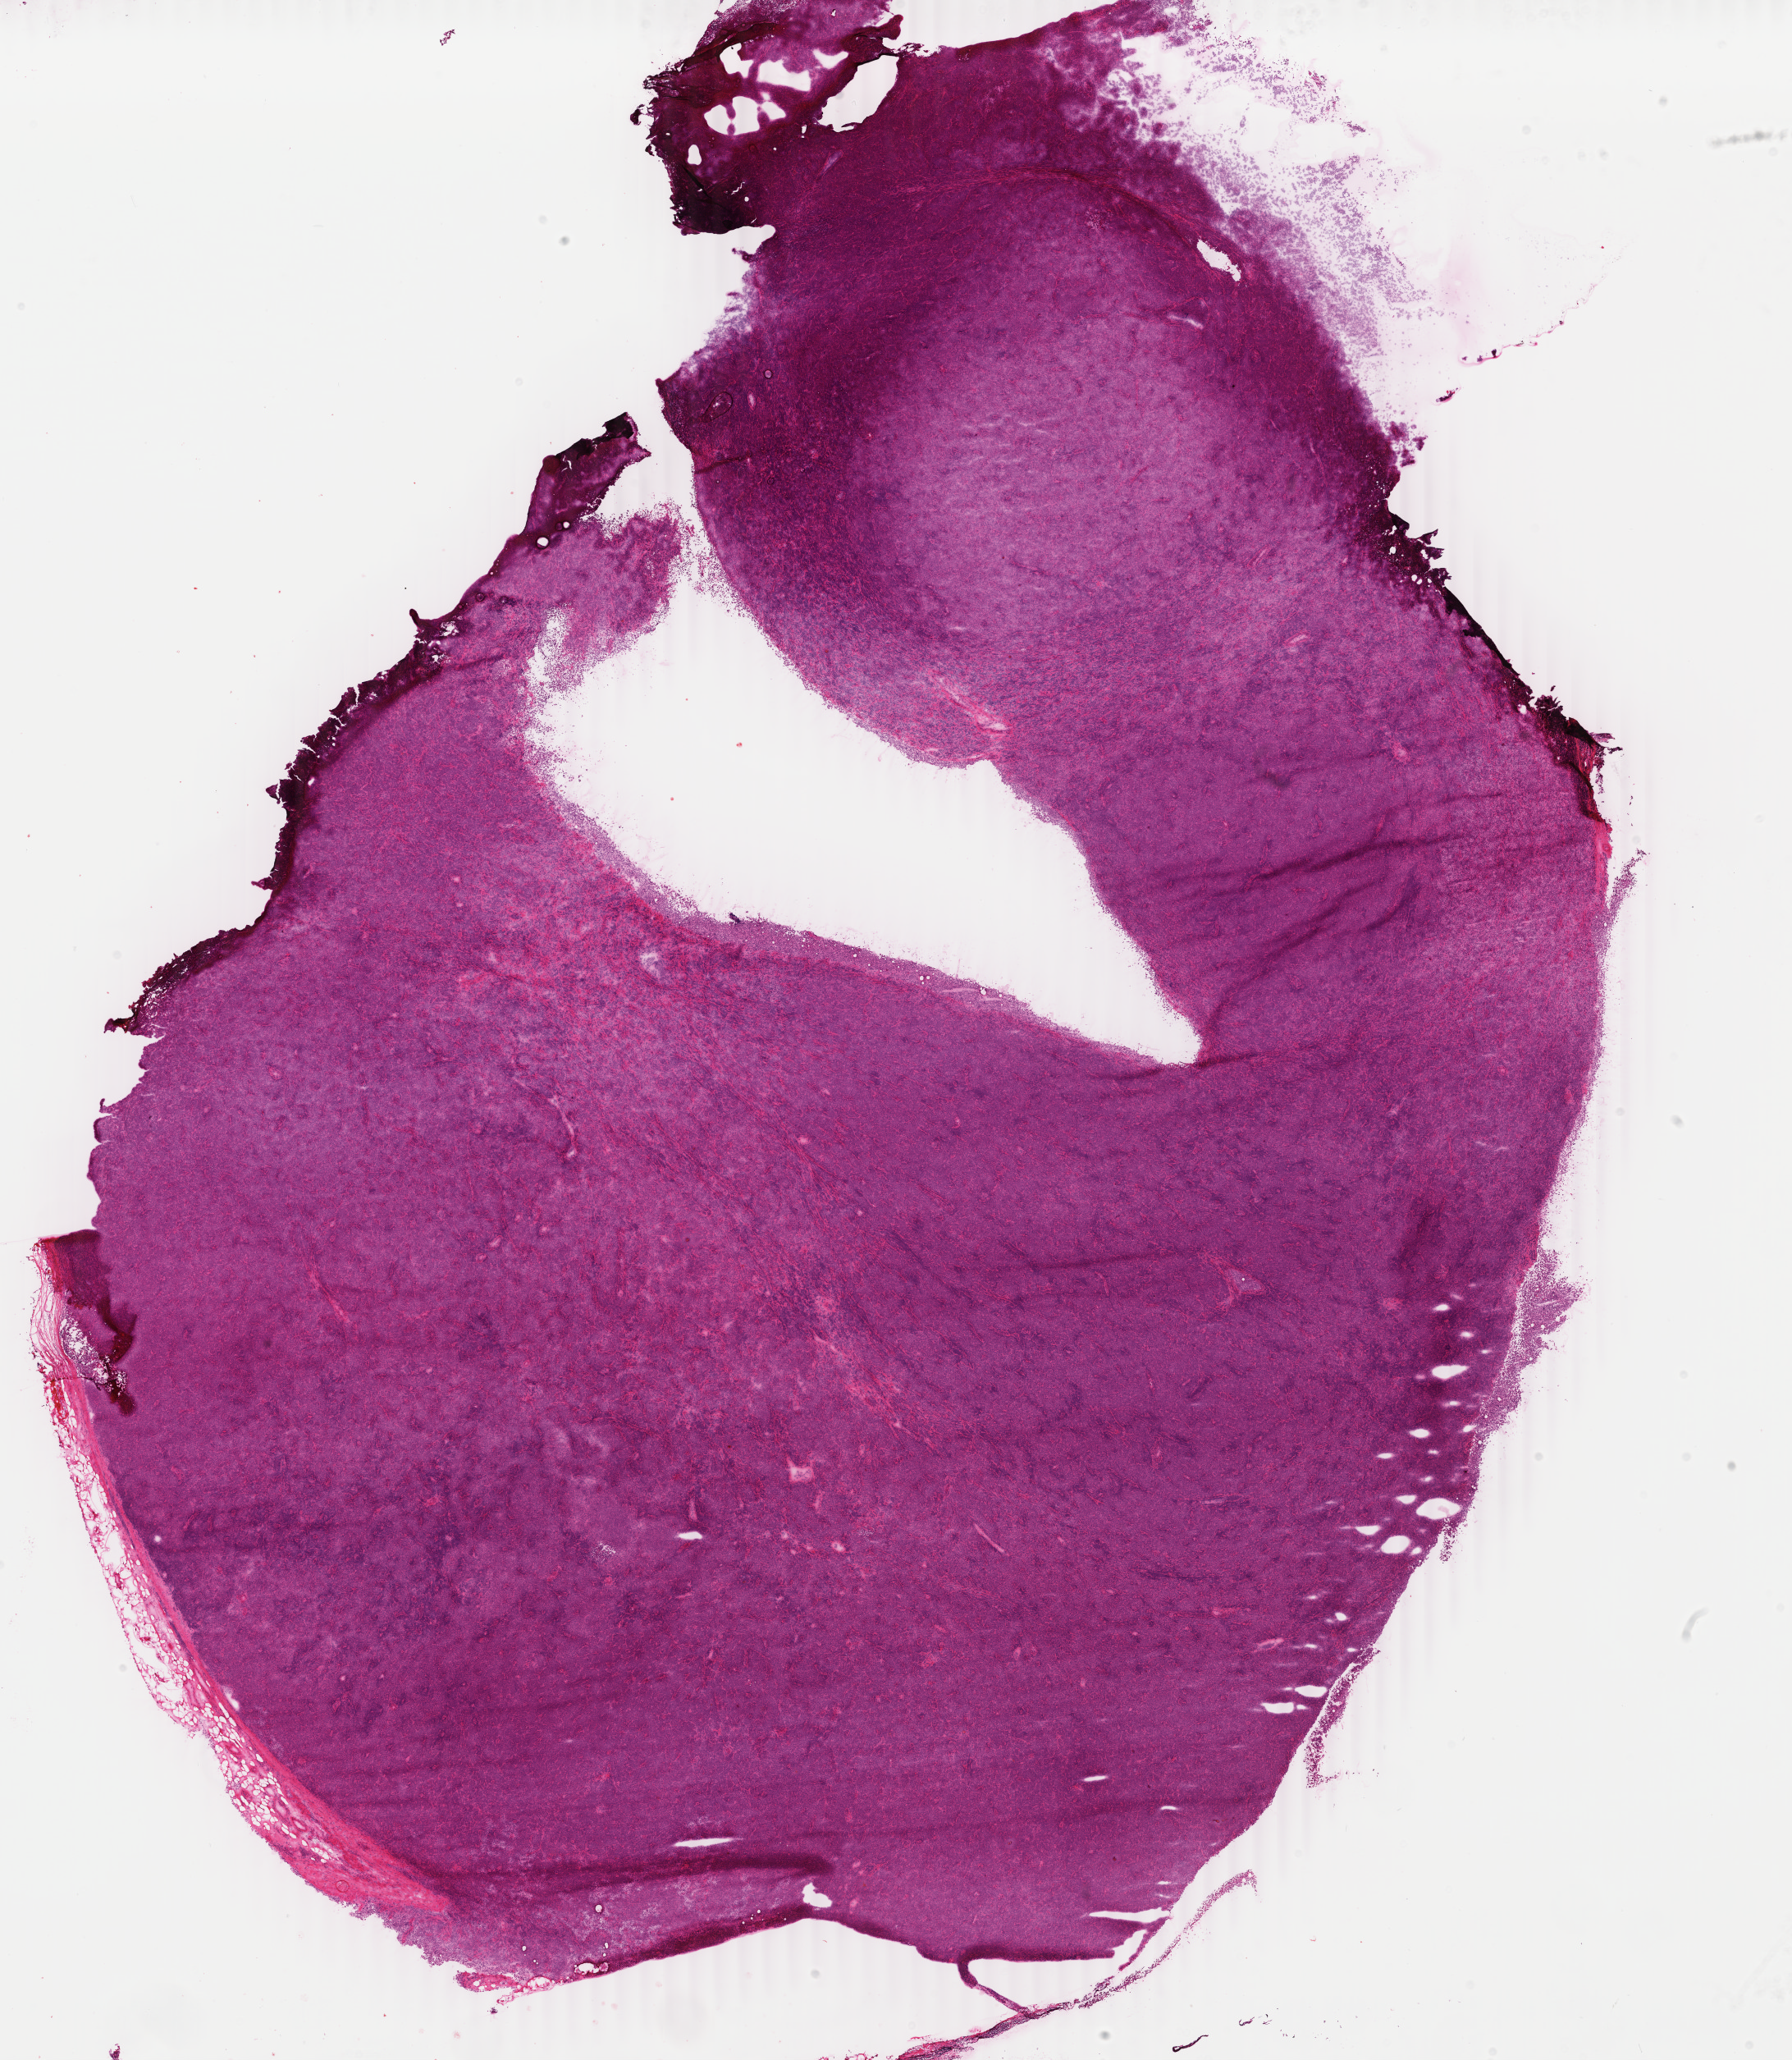
H&E whole-slide image — whole scanned area (about 17.4 x 20.0 mm) shown as a low-resolution overview; frozen section from the top of the tissue portion; primary tumour sample from the lymphoid tissue. Patient: female, age at initial diagnosis 54 years. Slide review estimates, as recorded: tumour cells 80%, tumour nuclei 85%, normal cells 13%, stromal cells 5%, necrosis 2%. Infiltration values recorded for this section: lymphocyte infiltration 13%, monocyte infiltration 2%, neutrophil infiltration 0%.
Pathologic diagnosis: Diffuse large B-cell lymphoma, NOS (lymph nodes of head, face and neck).